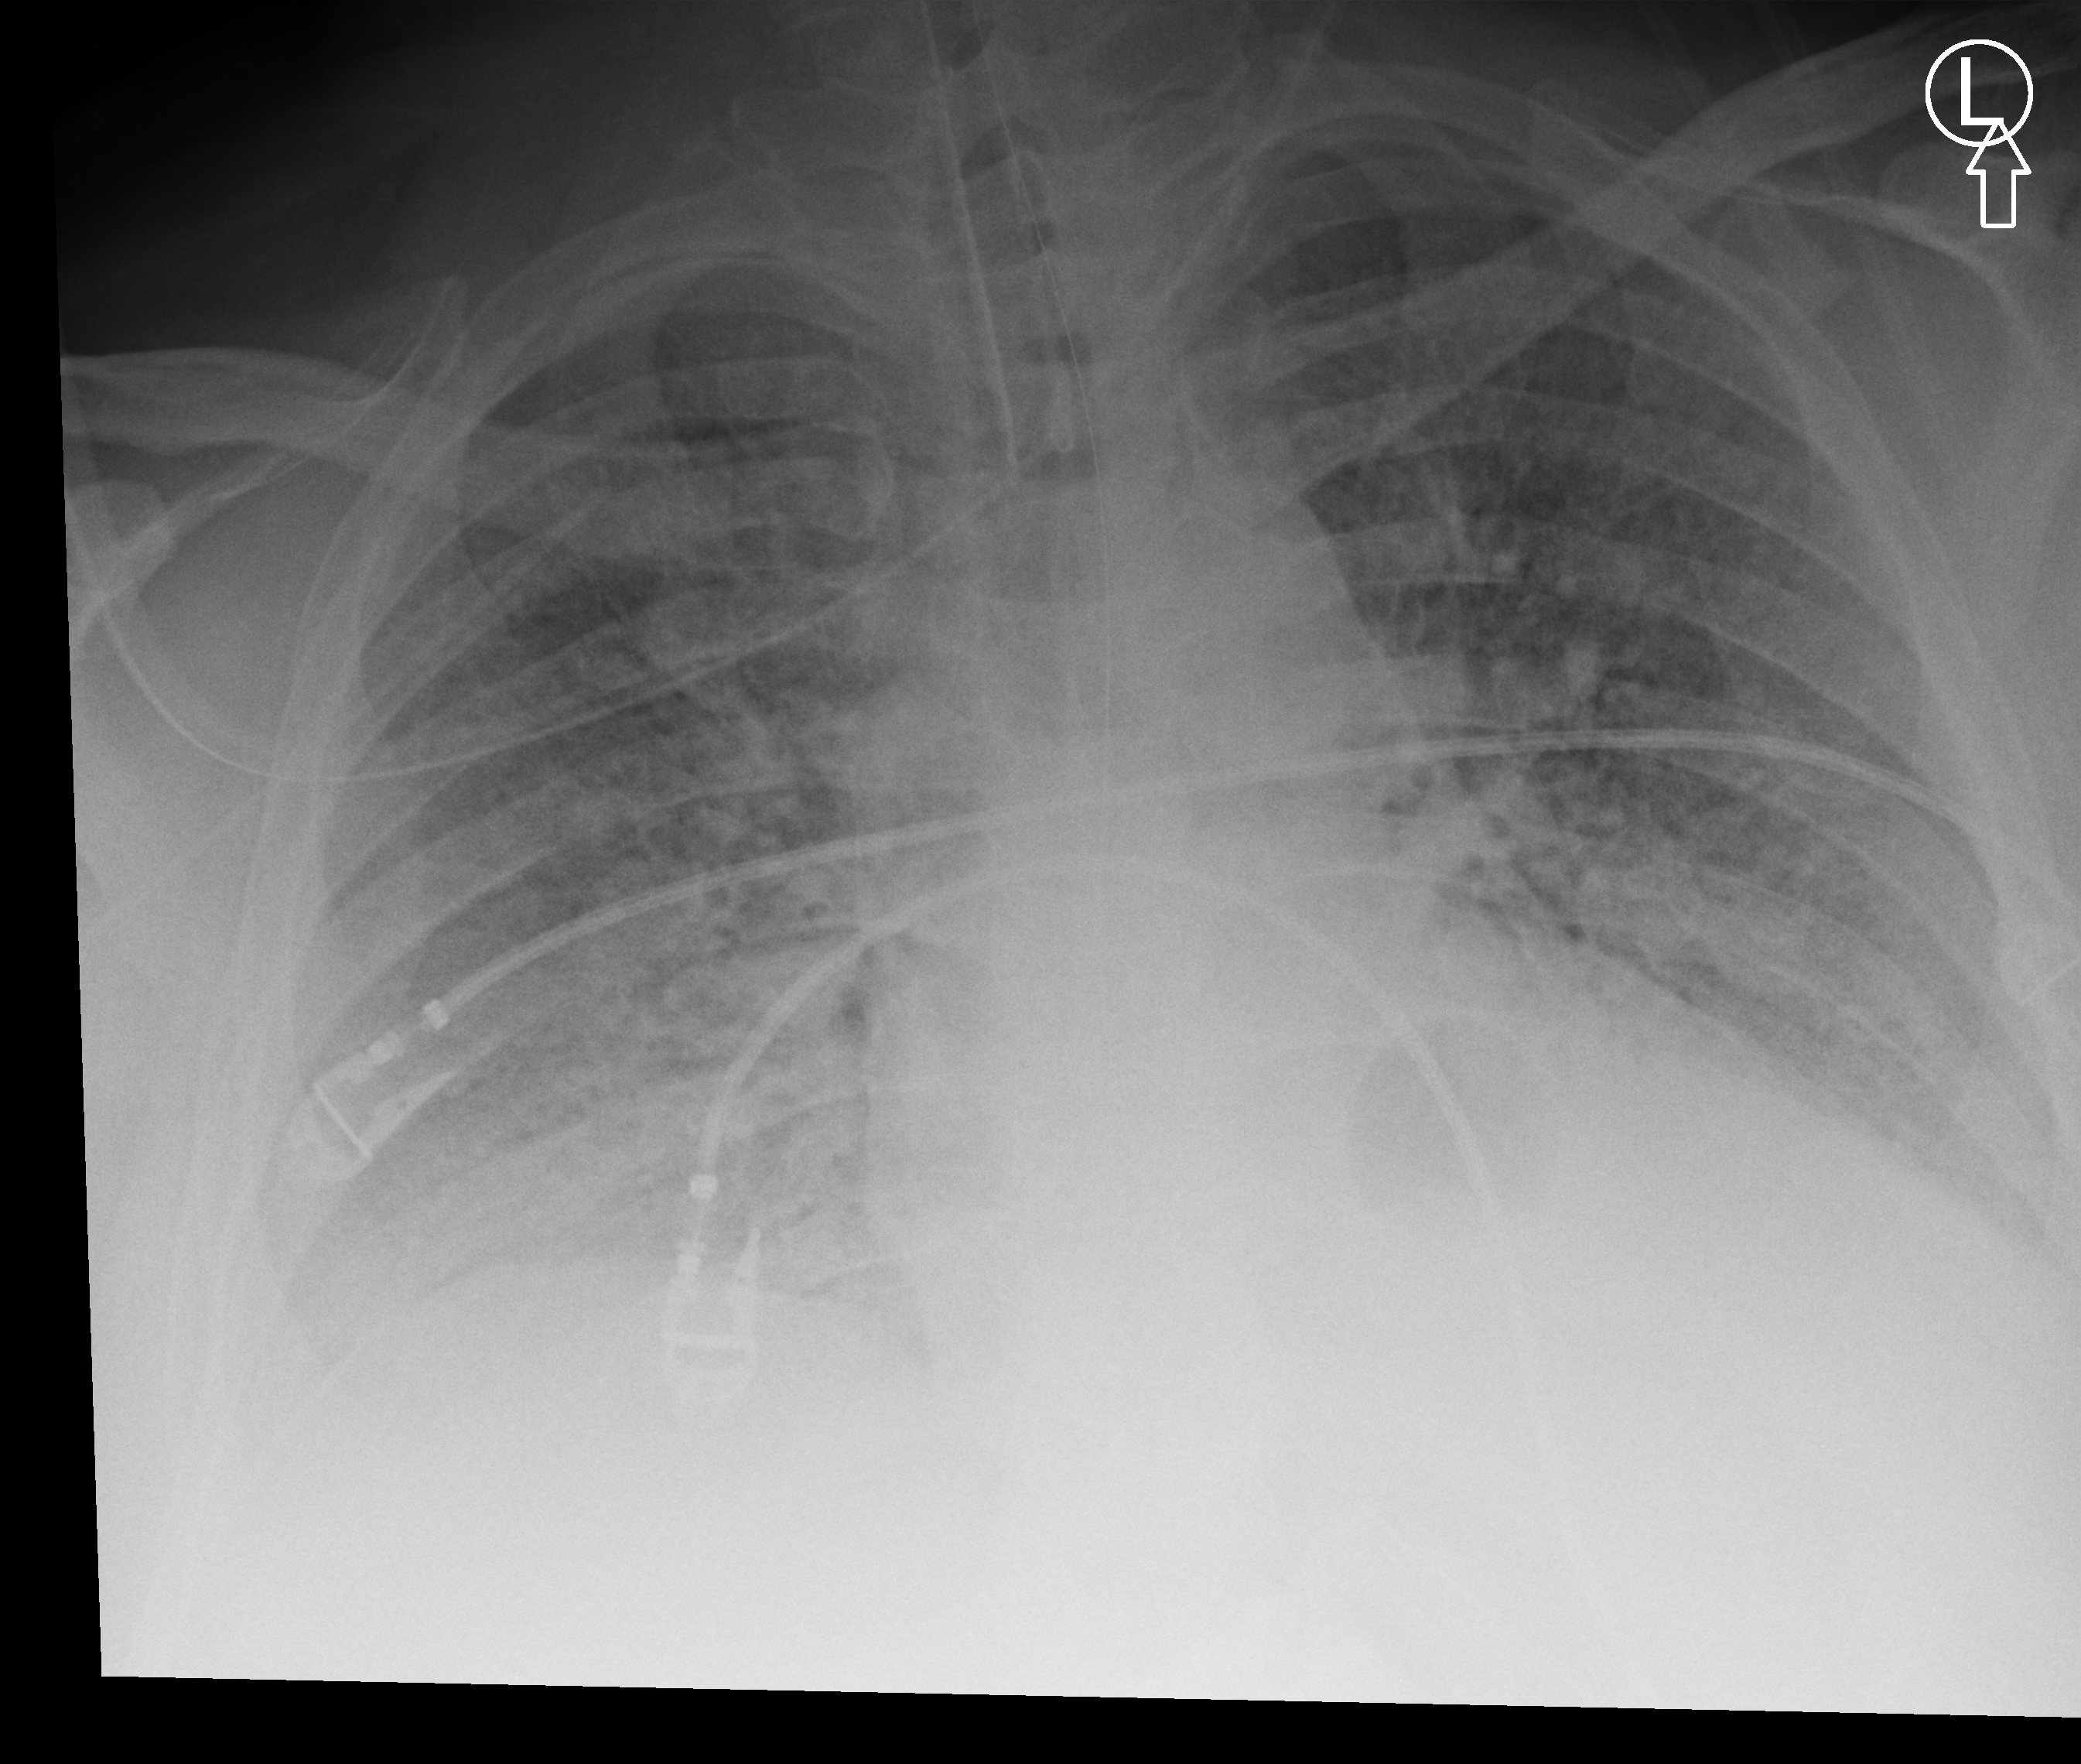
Chest X-ray (portable), anteroposterior (AP) projection. Adult patient hospitalised with COVID-19, age 18–59 years.
From the hospital-stay record, not from the radiograph (when in the stay this image was taken is not recorded):
- other chronic lung disease (admission record): no
- length of hospital stay: 26 days